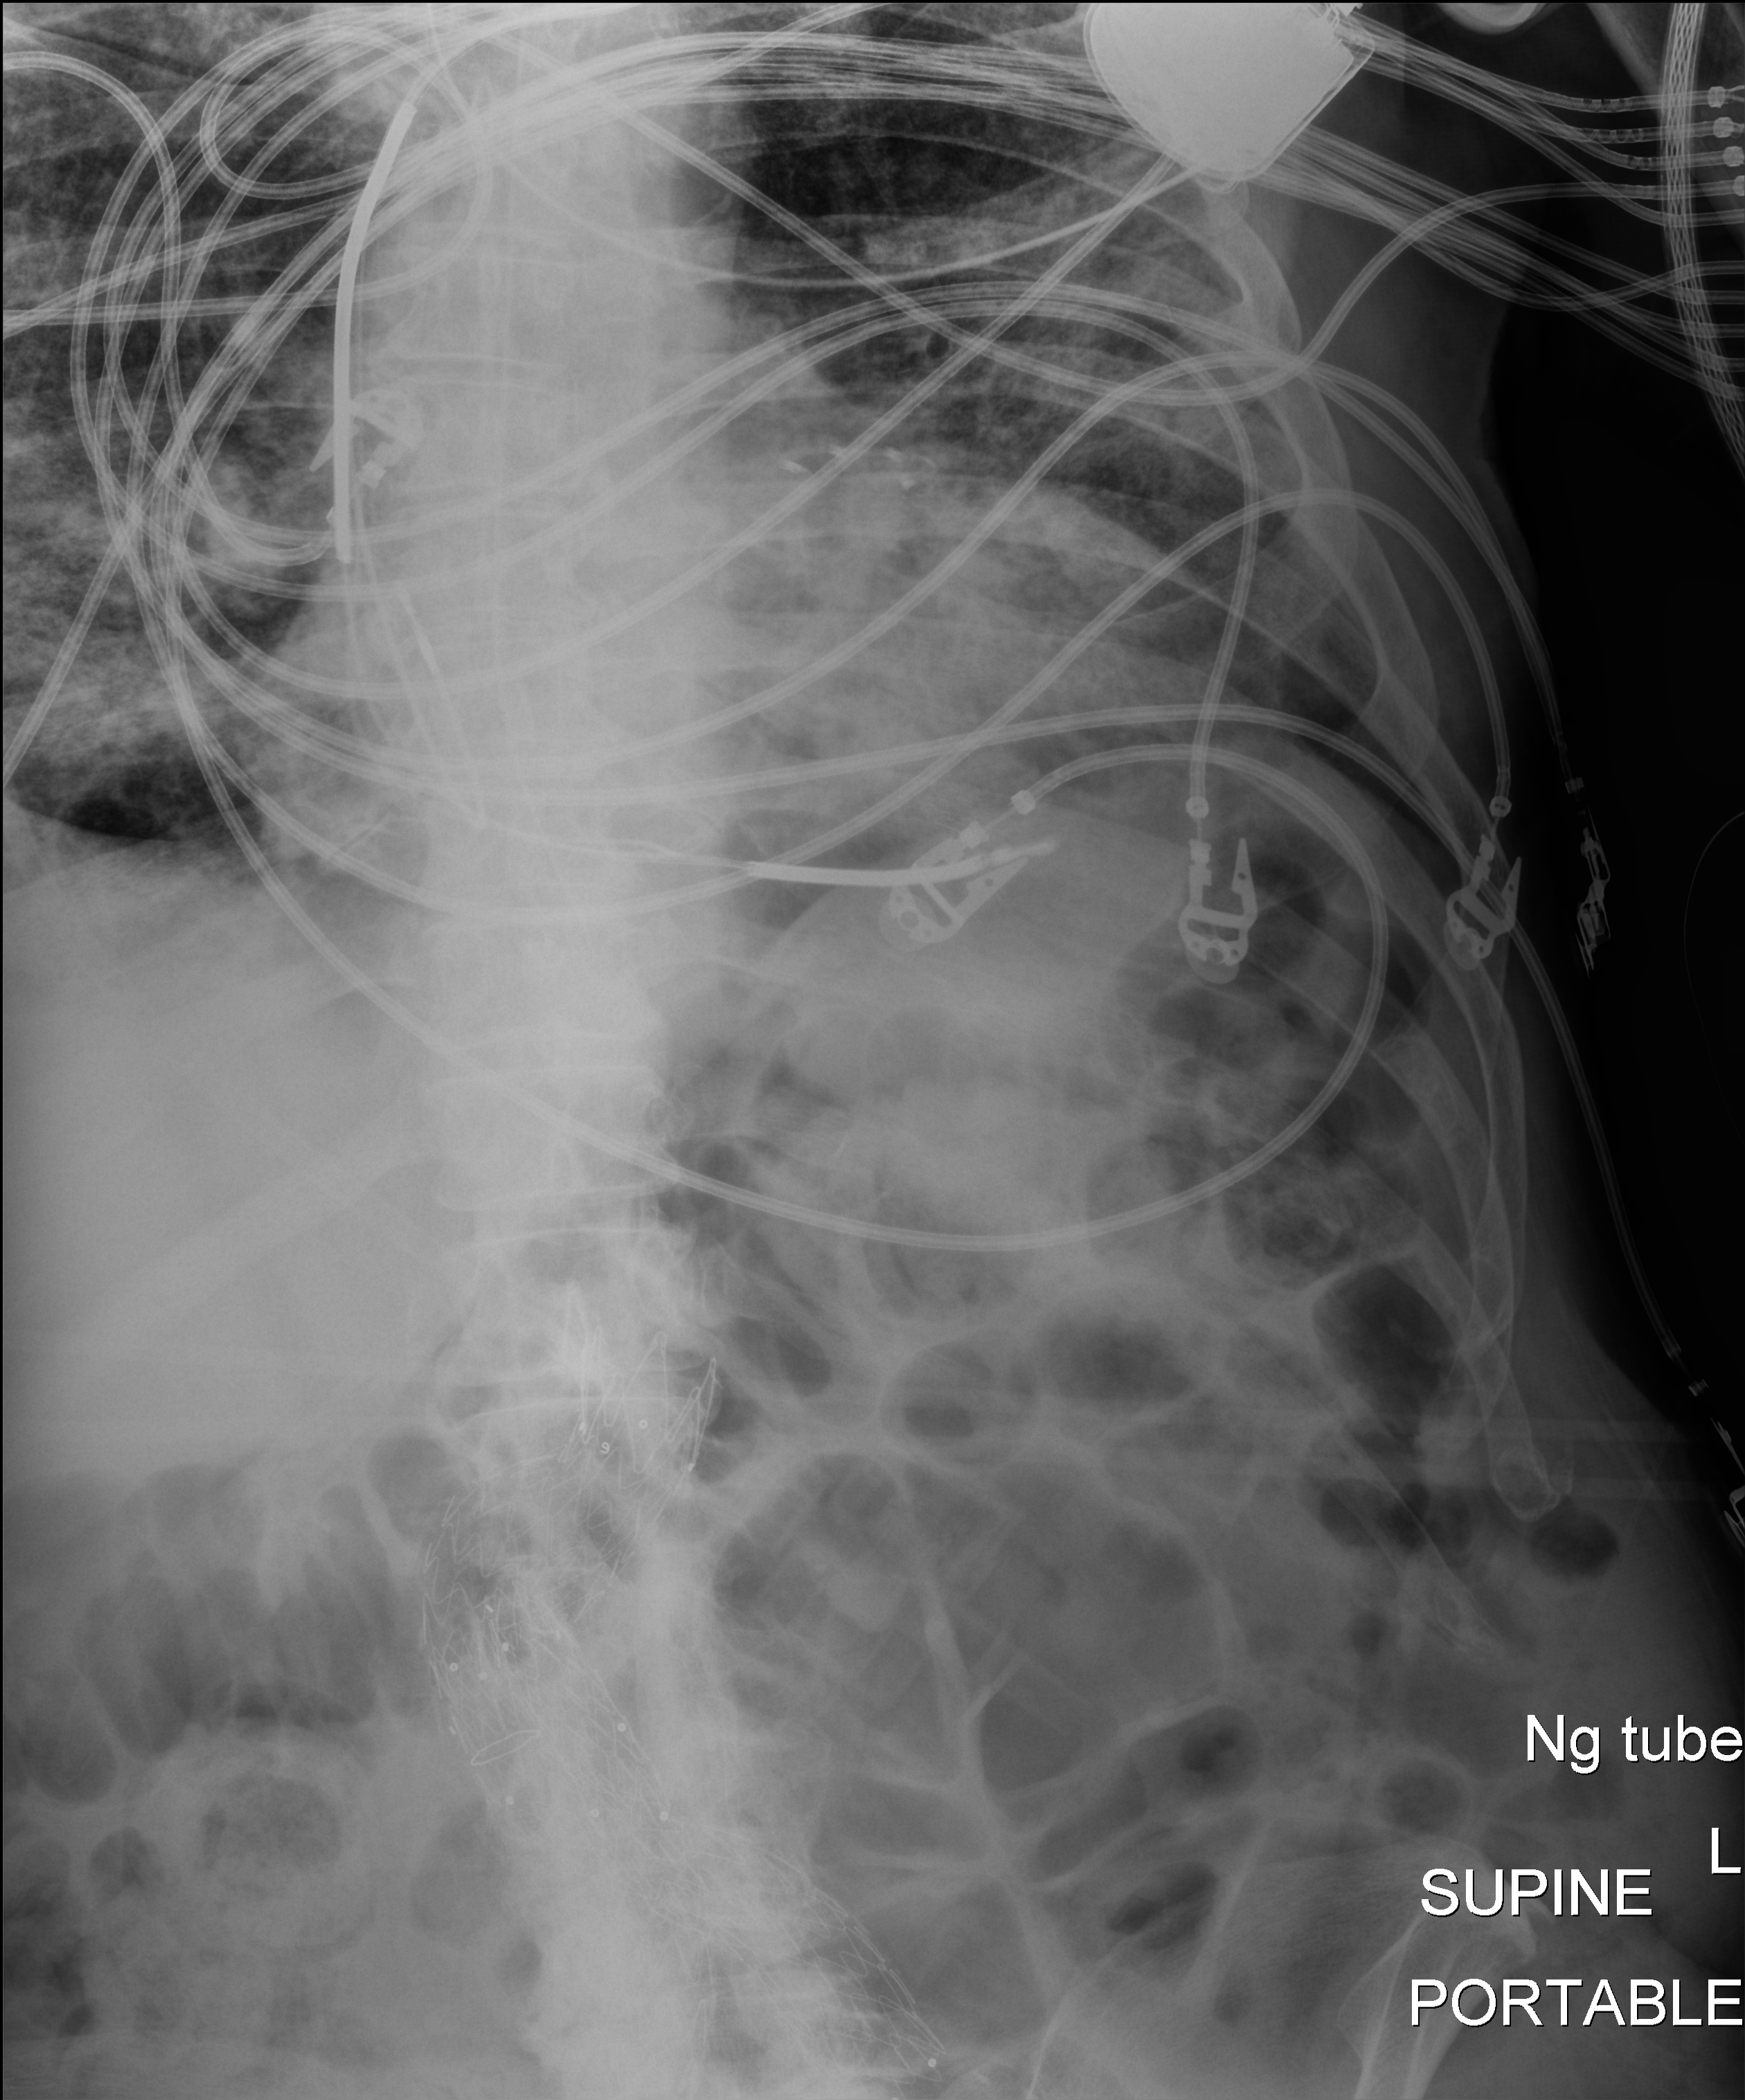
Abdomen X-ray (portable), anteroposterior (AP) projection. Patient hospitalised with COVID-19; male, aged 60–74 years.
Admission-level facts for this patient (not findings on this image; timing relative to this image not recorded):
- hypertension (admission record): yes
- admitted to intensive care during this hospital stay: yes